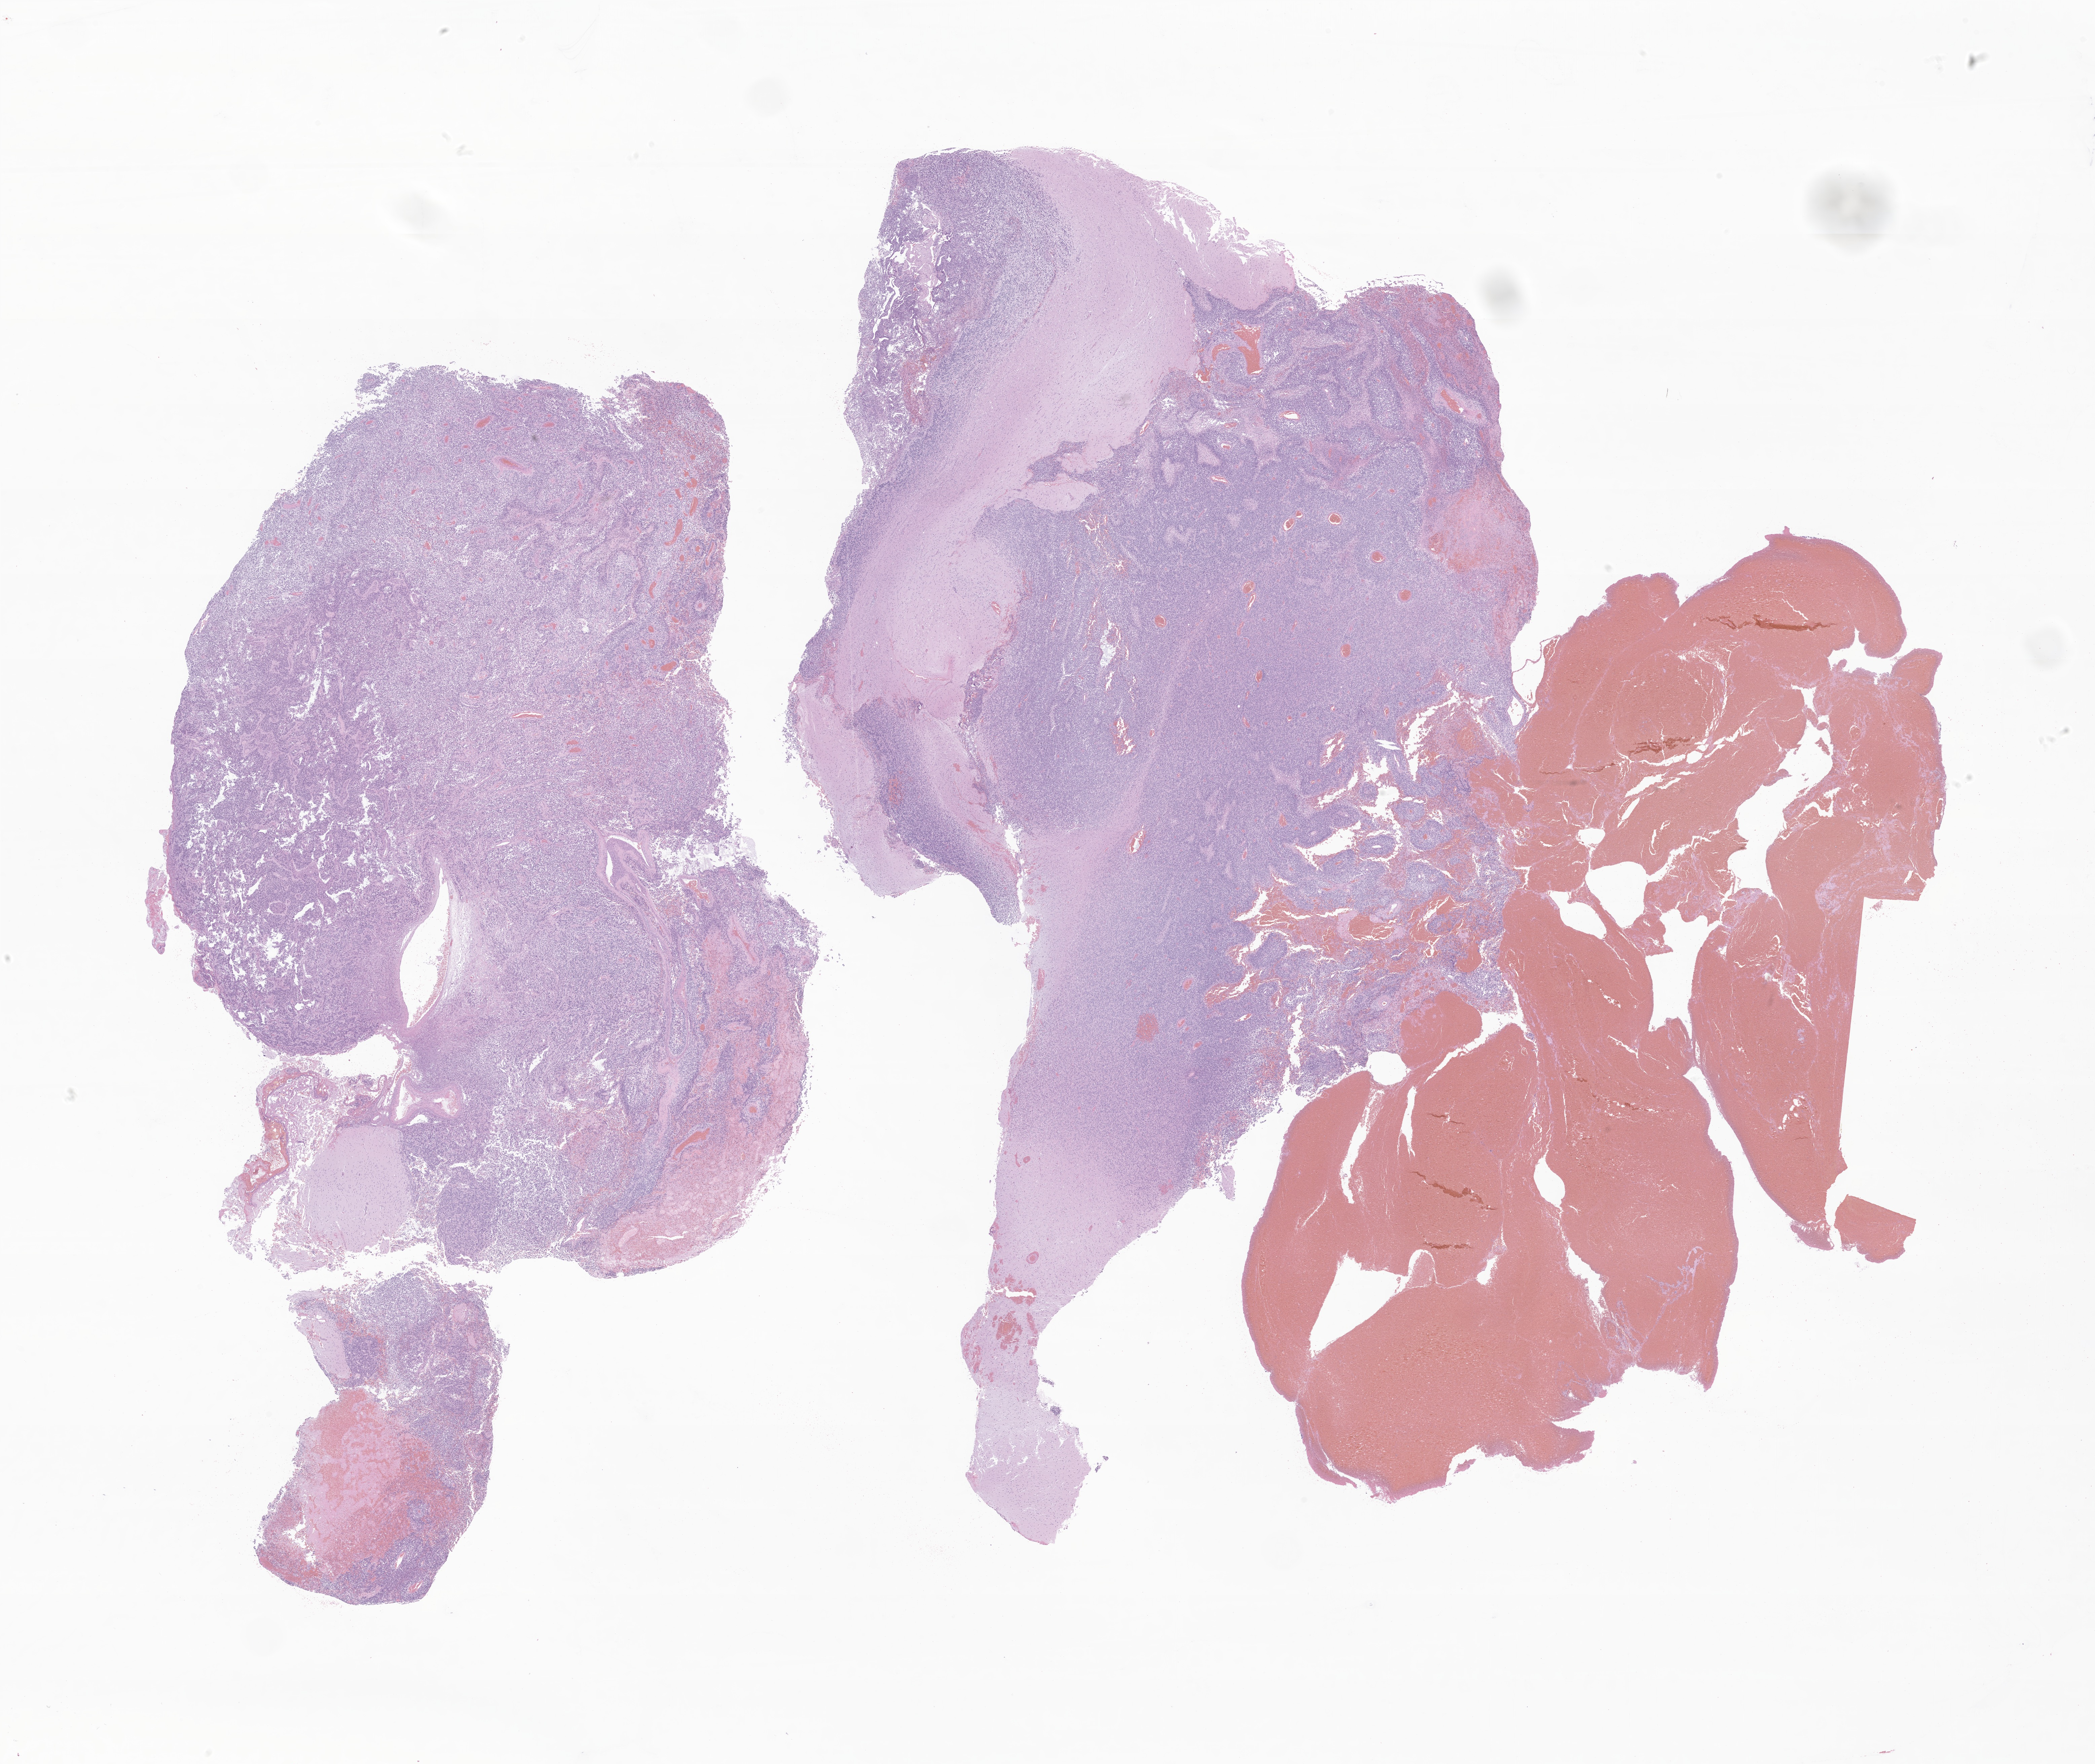
Whole-slide image, H&E stain of tumor tissue from the brain — a low-resolution overview of the entire scanned area, about 26.3 x 22.1 mm; formalin-fixed paraffin-embedded section. Male patient, age 170 months (14 years 2 months).
• recorded diagnosis: Pleomorphic xanthoastrocytoma, NOS